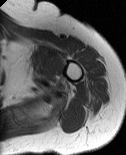
MRI of an extremity soft-tissue mass, one axial slice. Position 65 of 86 along the scan axis. MR volume resampled by the dataset authors to the PET/CT grid (not the native acquisition matrix). 126 × 155 image matrix, field of view 123 × 151 mm. Female patient. From the clinical record (not read from this slice): histological type: pleiomorphic leiomyosarcoma; grade: high; site of the primary tumour: left biceps.
Annotated regions visible in this slice (expert contour drawn on MRI and transferred to this co-registered scan by the dataset authors):
- gross tumour volume including surrounding oedema: bounding box [x1, y1, x2, y2] px = [31, 49, 55, 91]